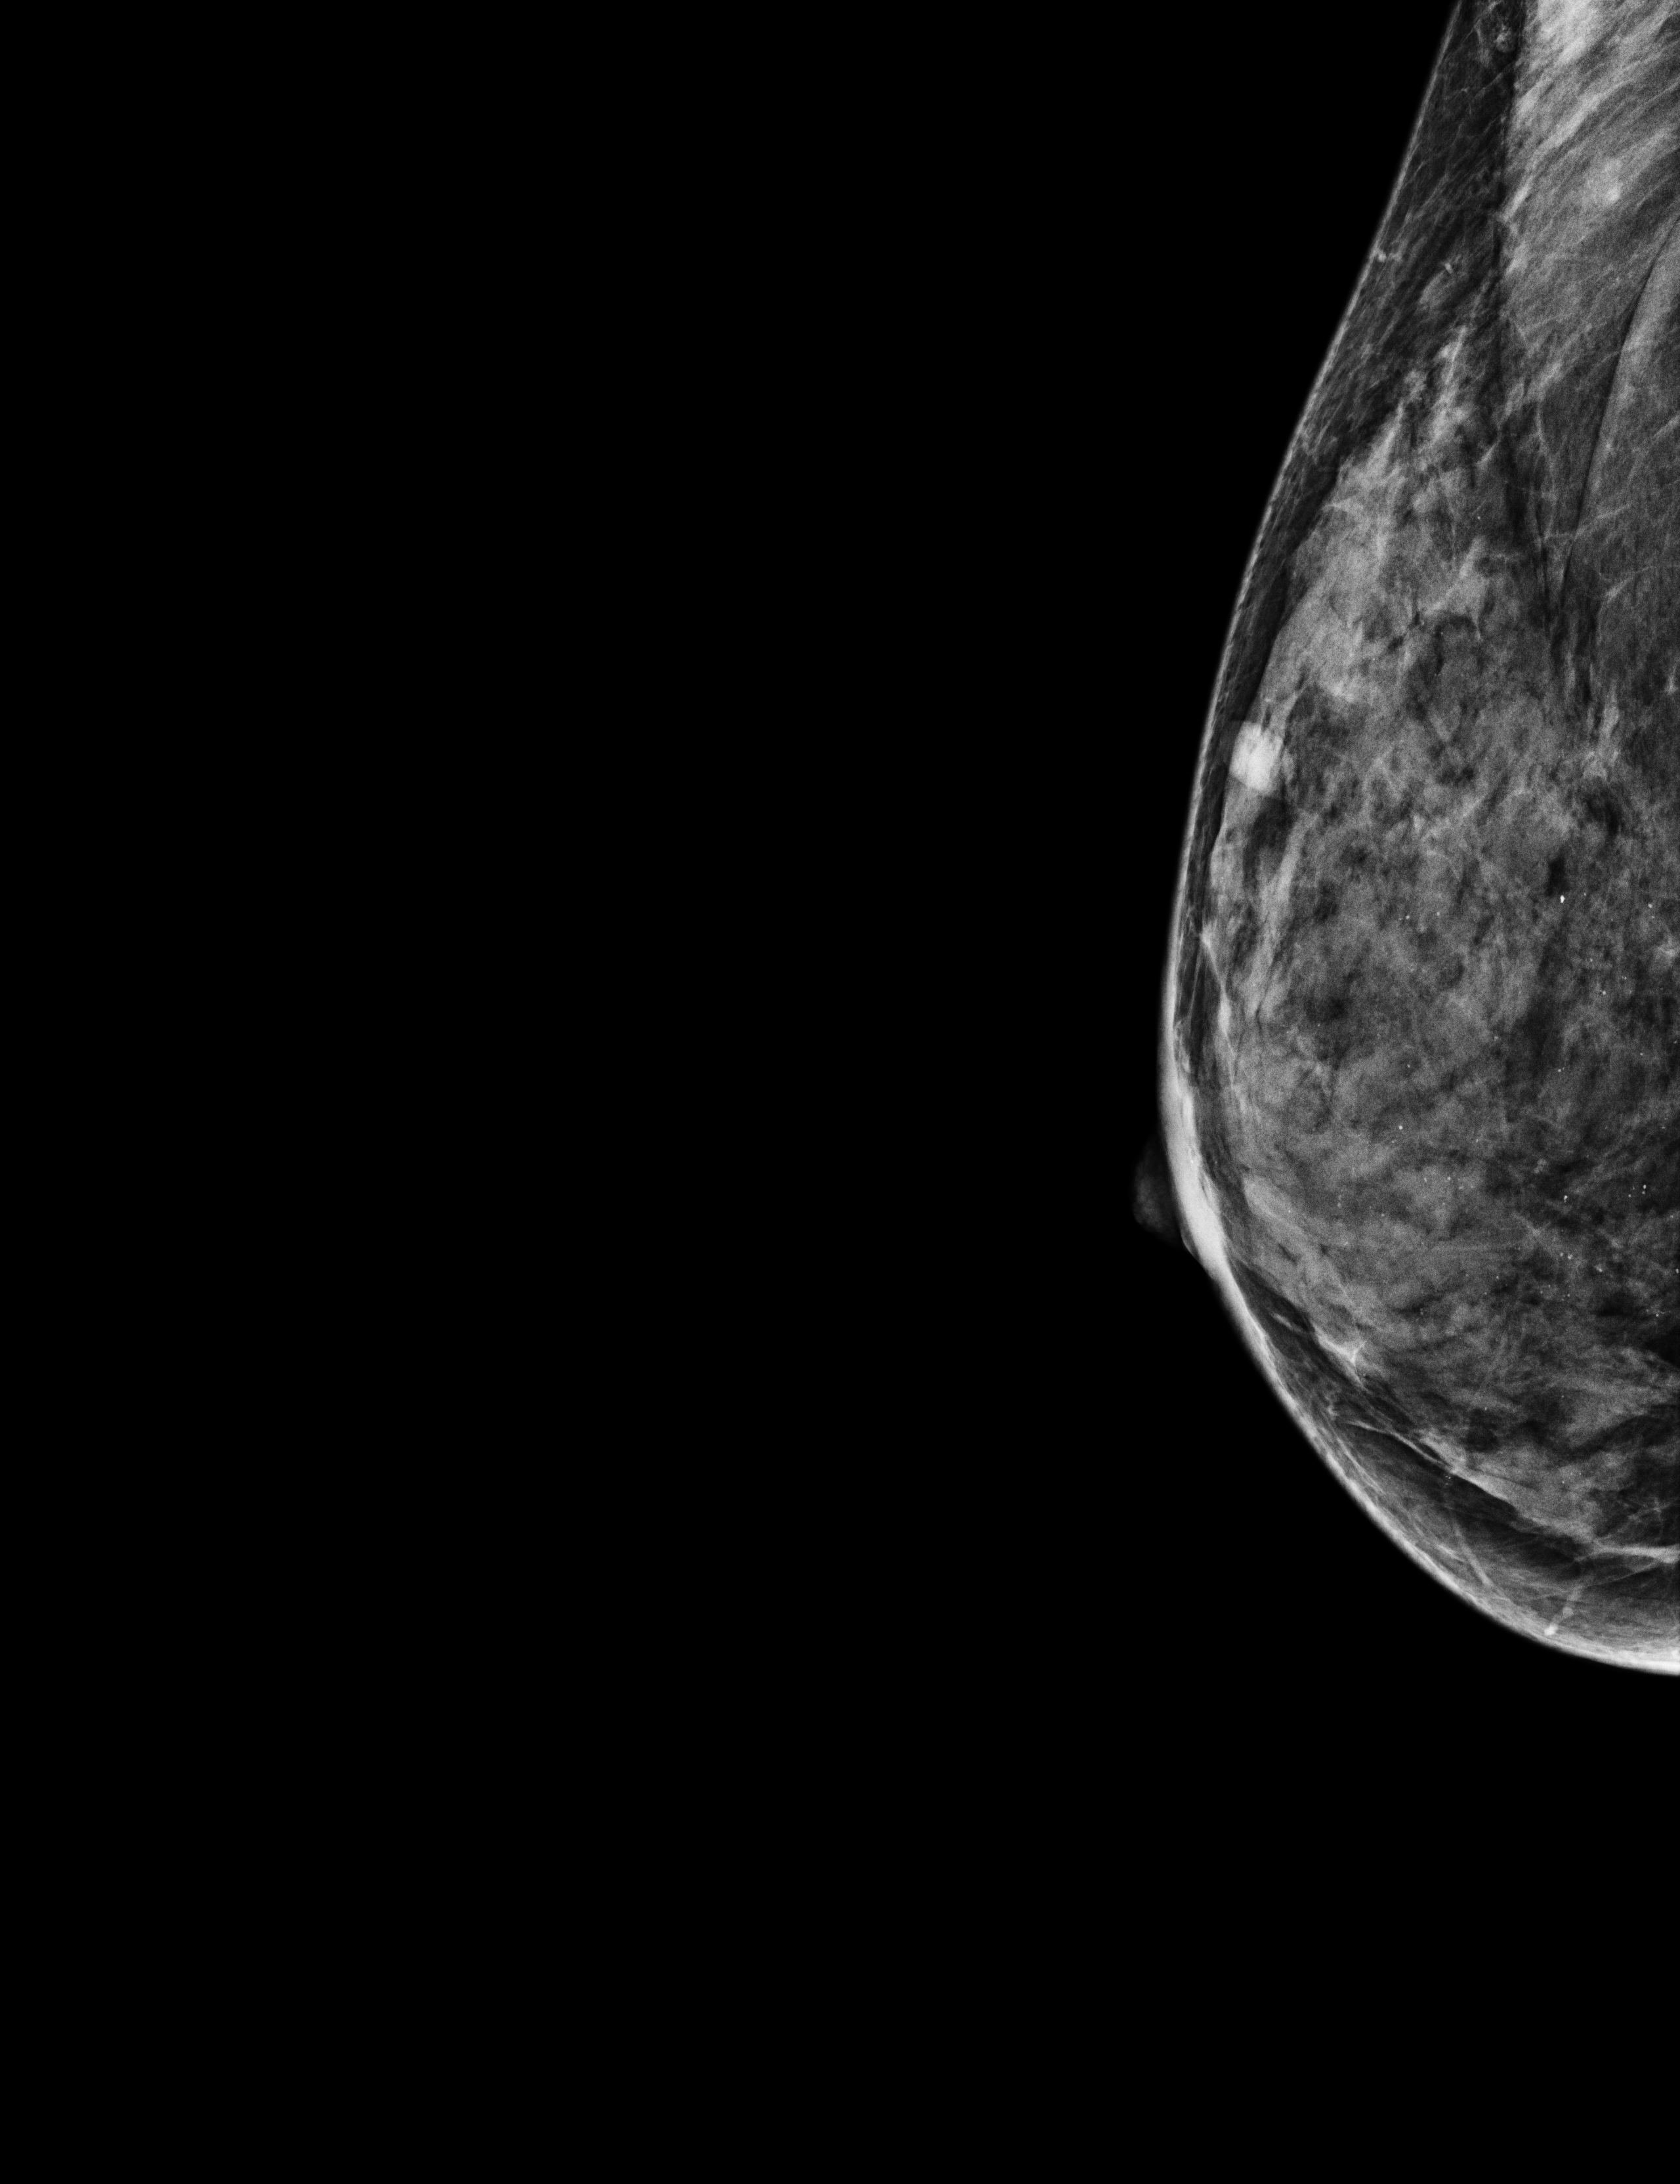
Annual screening mammography examination, system: Selenia Dimensions. Patient aged 50 years (female).
Image type: full-field digital mammogram. Breast: right. Projection: laterally exaggerated craniocaudal (XCCL) view.